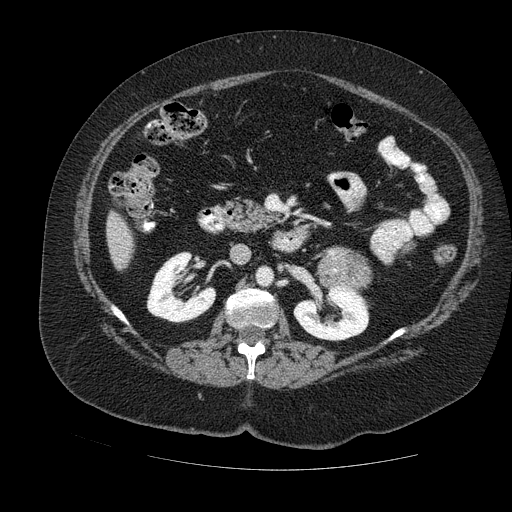
Contrast-enhanced abdominal CT, one axial slice. Position 56 of 121 along the scan axis. Soft-tissue window (W 400 / L 40 HU). 512 × 512 image matrix, field of view 420 × 420 mm. Female patient. Case-level facts recorded for this patient, not image findings: diagnosis: adrenocortical carcinoma; tumour side: left adrenal; tumour size at pathology: 8 cm.
Outlined on this slice (semi-automatically segmented with operator editing):
- mass: bounding box <321,250,371,285> (left, top, right, bottom; pixels)